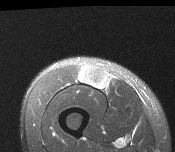
MRI of an extremity soft-tissue mass, one axial slice. Slice 45 of 116 in the series (ordered by position). T2-weighted fat-saturated. MR volume resampled by the dataset authors to the PET/CT grid (not the native acquisition matrix). 3.27 mm slice thickness. 175 × 152 image matrix, field of view 171 × 148 mm. Male patient. Case-level facts recorded for this patient, not image findings: histological type: pleiomorphic leiomyosarcoma; grade: intermediate; site of the primary tumour: right thigh.
Outlined on this slice (expert contour drawn on MRI and transferred to this co-registered scan by the dataset authors):
- gross tumour volume including surrounding oedema: bounding box (x1, y1, x2, y2) in pixels: (79, 67, 110, 89)